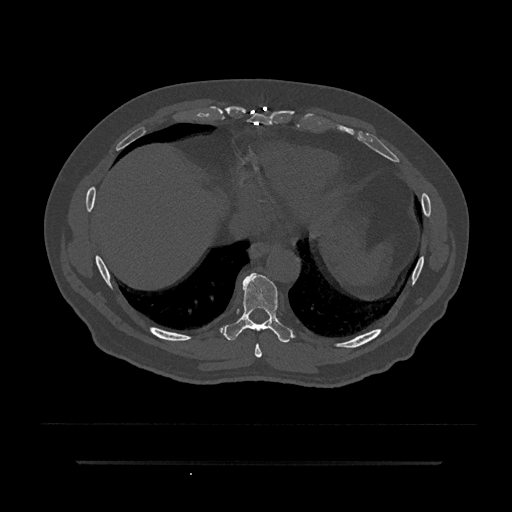
CT including the spine, one axial slice; slice 384 of 797 in the series (ordered by position); 120 kVp; bone window (W 1800 / L 400 HU); 0.5 mm slice thickness; 512 × 512 image matrix, field of view 464 × 464 mm. Patient: male, 59 years. From the clinical record (not read from this slice): primary cancer: bile ducts.
Outlined on this slice (semi-automatic segmentation, software-assisted and operator-edited):
- T8 vertebra: bounding box [x1, y1, x2, y2] px = [255, 344, 262, 358]
- T9 vertebra: [222, 273, 292, 343]